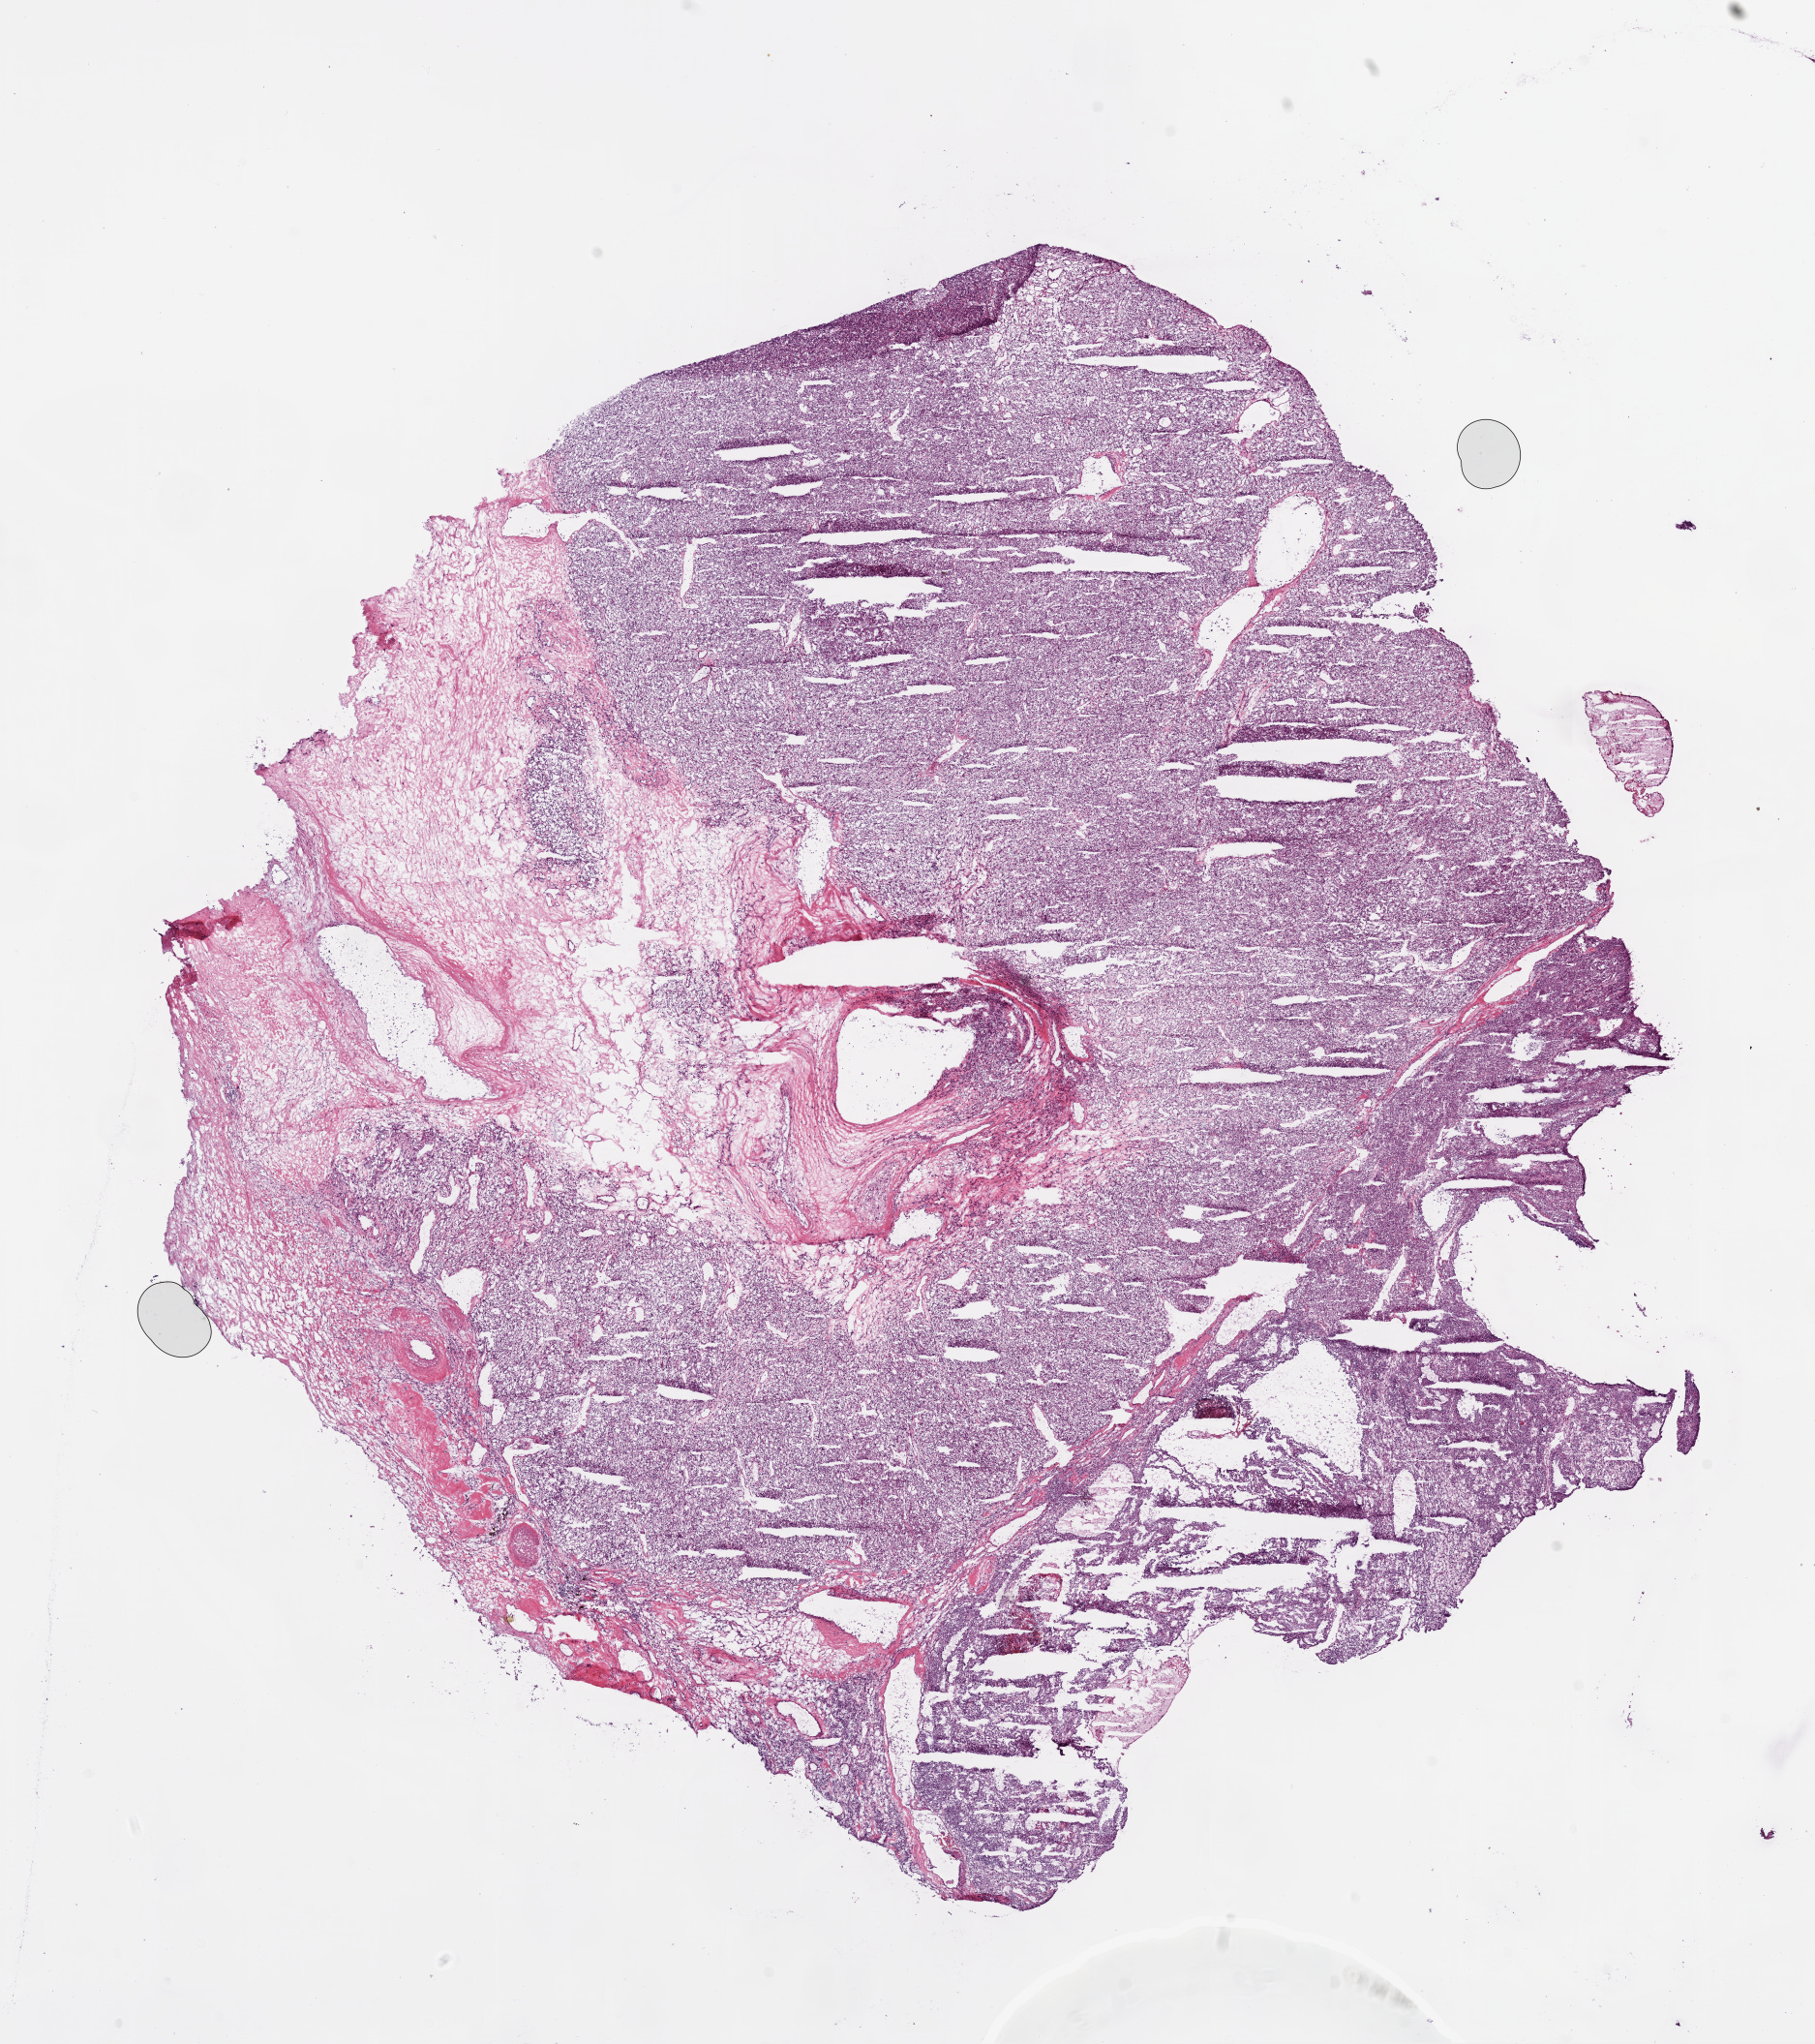
Hematoxylin and eosin (H&E) stained whole-slide image, low-resolution overview of the scanned area, about 15.0 x 16.9 mm (slide scanned at 20x); frozen section from the bottom of the tissue portion; primary tumour sample from the kidney. Female patient; age at initial diagnosis 68 years. Histologic grade: G2 (moderately differentiated). Slide review estimates, as recorded: tumour cells 85%, tumour nuclei 85%, normal cells 0%, stromal cells 15%, necrosis 0%.
AJCC pathologic stage: I. Diagnosis: Clear cell adenocarcinoma, NOS.